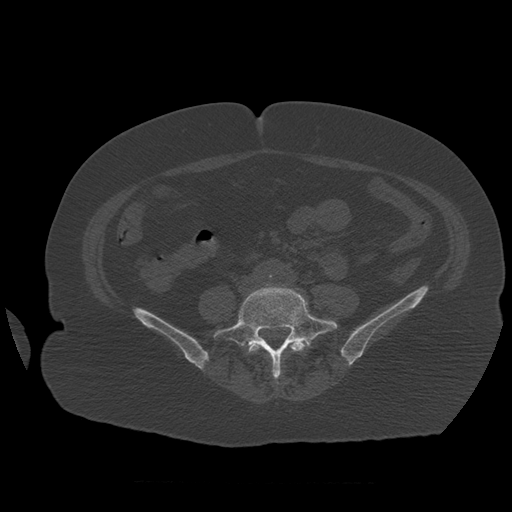
CT including the spine, one axial slice. Reconstruction kernel STANDARD. 120 kVp. Bone window (W 1800 / L 400 HU). 512 × 512 image matrix. Patient age 81 years. Case-level facts recorded for this patient, not image findings: primary cancer: renal; vertebrae with lytic lesions (as recorded): L1.
Structures marked on this image (semi-automatically segmented with operator editing):
- L4 vertebra: bounding box (x1, y1, x2, y2) in pixels: (247, 337, 309, 380)
- L5 vertebra: (214, 284, 338, 384)